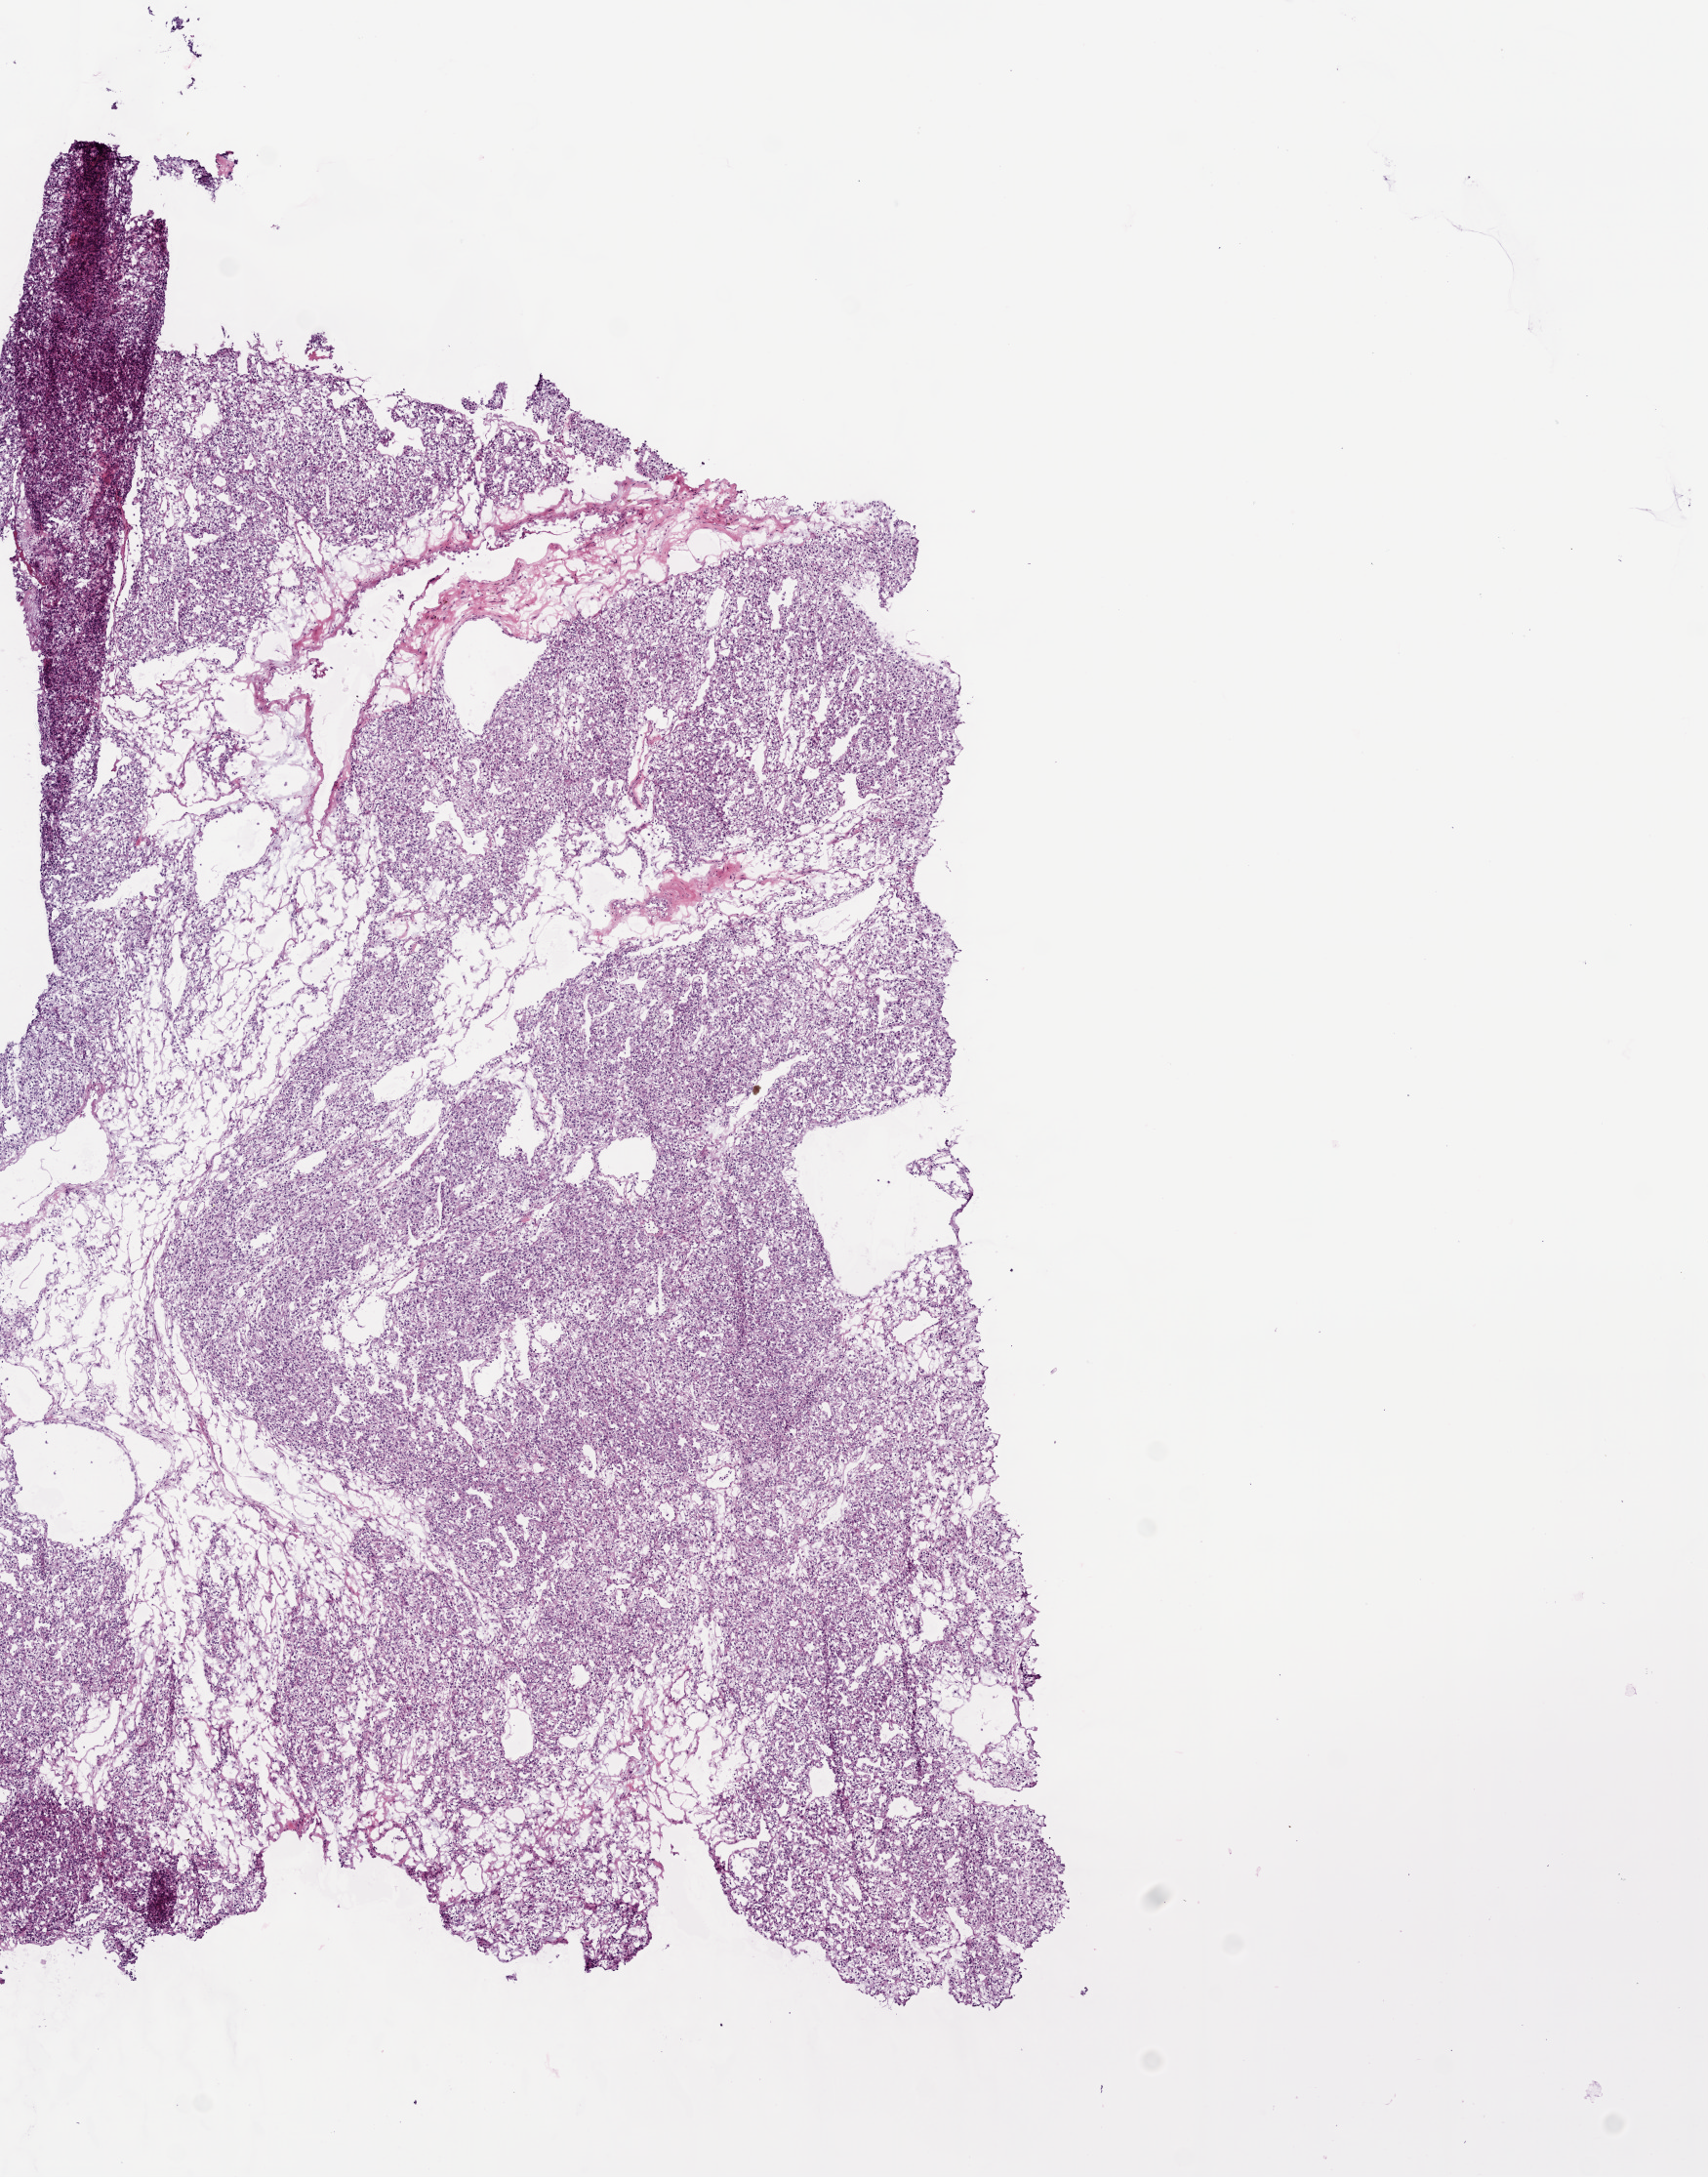
Whole-slide histology image, Hematoxylin and eosin (H&E) stained, a low-resolution overview of the entire scanned area, about 7.0 x 8.9 mm (slide scanned at 20x), frozen section from the bottom of the tissue portion, sample: primary tumour, kidney. Patient: male, age at initial diagnosis 64 years. Histologic grade: G2 (moderately differentiated). Slide review estimates, as recorded: tumour cells 90%, tumour nuclei 85%, normal cells 0%, stromal cells 10%, necrosis 0%.
Pathologic diagnosis: Clear cell adenocarcinoma, NOS. TNM: T3 NX M0. AJCC pathologic stage: III. Laterality: left.